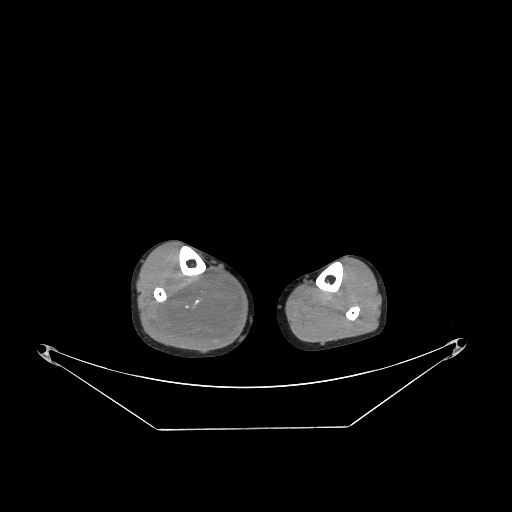
CT of an extremity soft-tissue mass (from a PET/CT study), one axial slice. Slice 100 of 267 in the series (ordered by position). Reconstruction kernel STANDARD. 140 kVp. Soft-tissue window (W 400 / L 40 HU). 512 × 512 image matrix, field of view 500 × 500 mm. Male patient. Case-level facts recorded for this patient, not image findings: histological type: liposarcoma - round cell; grade: high; site of the primary tumour: right calf.
Annotated regions visible in this slice (expert contour drawn on MRI and transferred to this co-registered scan by the dataset authors):
- gross tumour volume (mass): box from (x=153, y=270) to (x=241, y=346) px